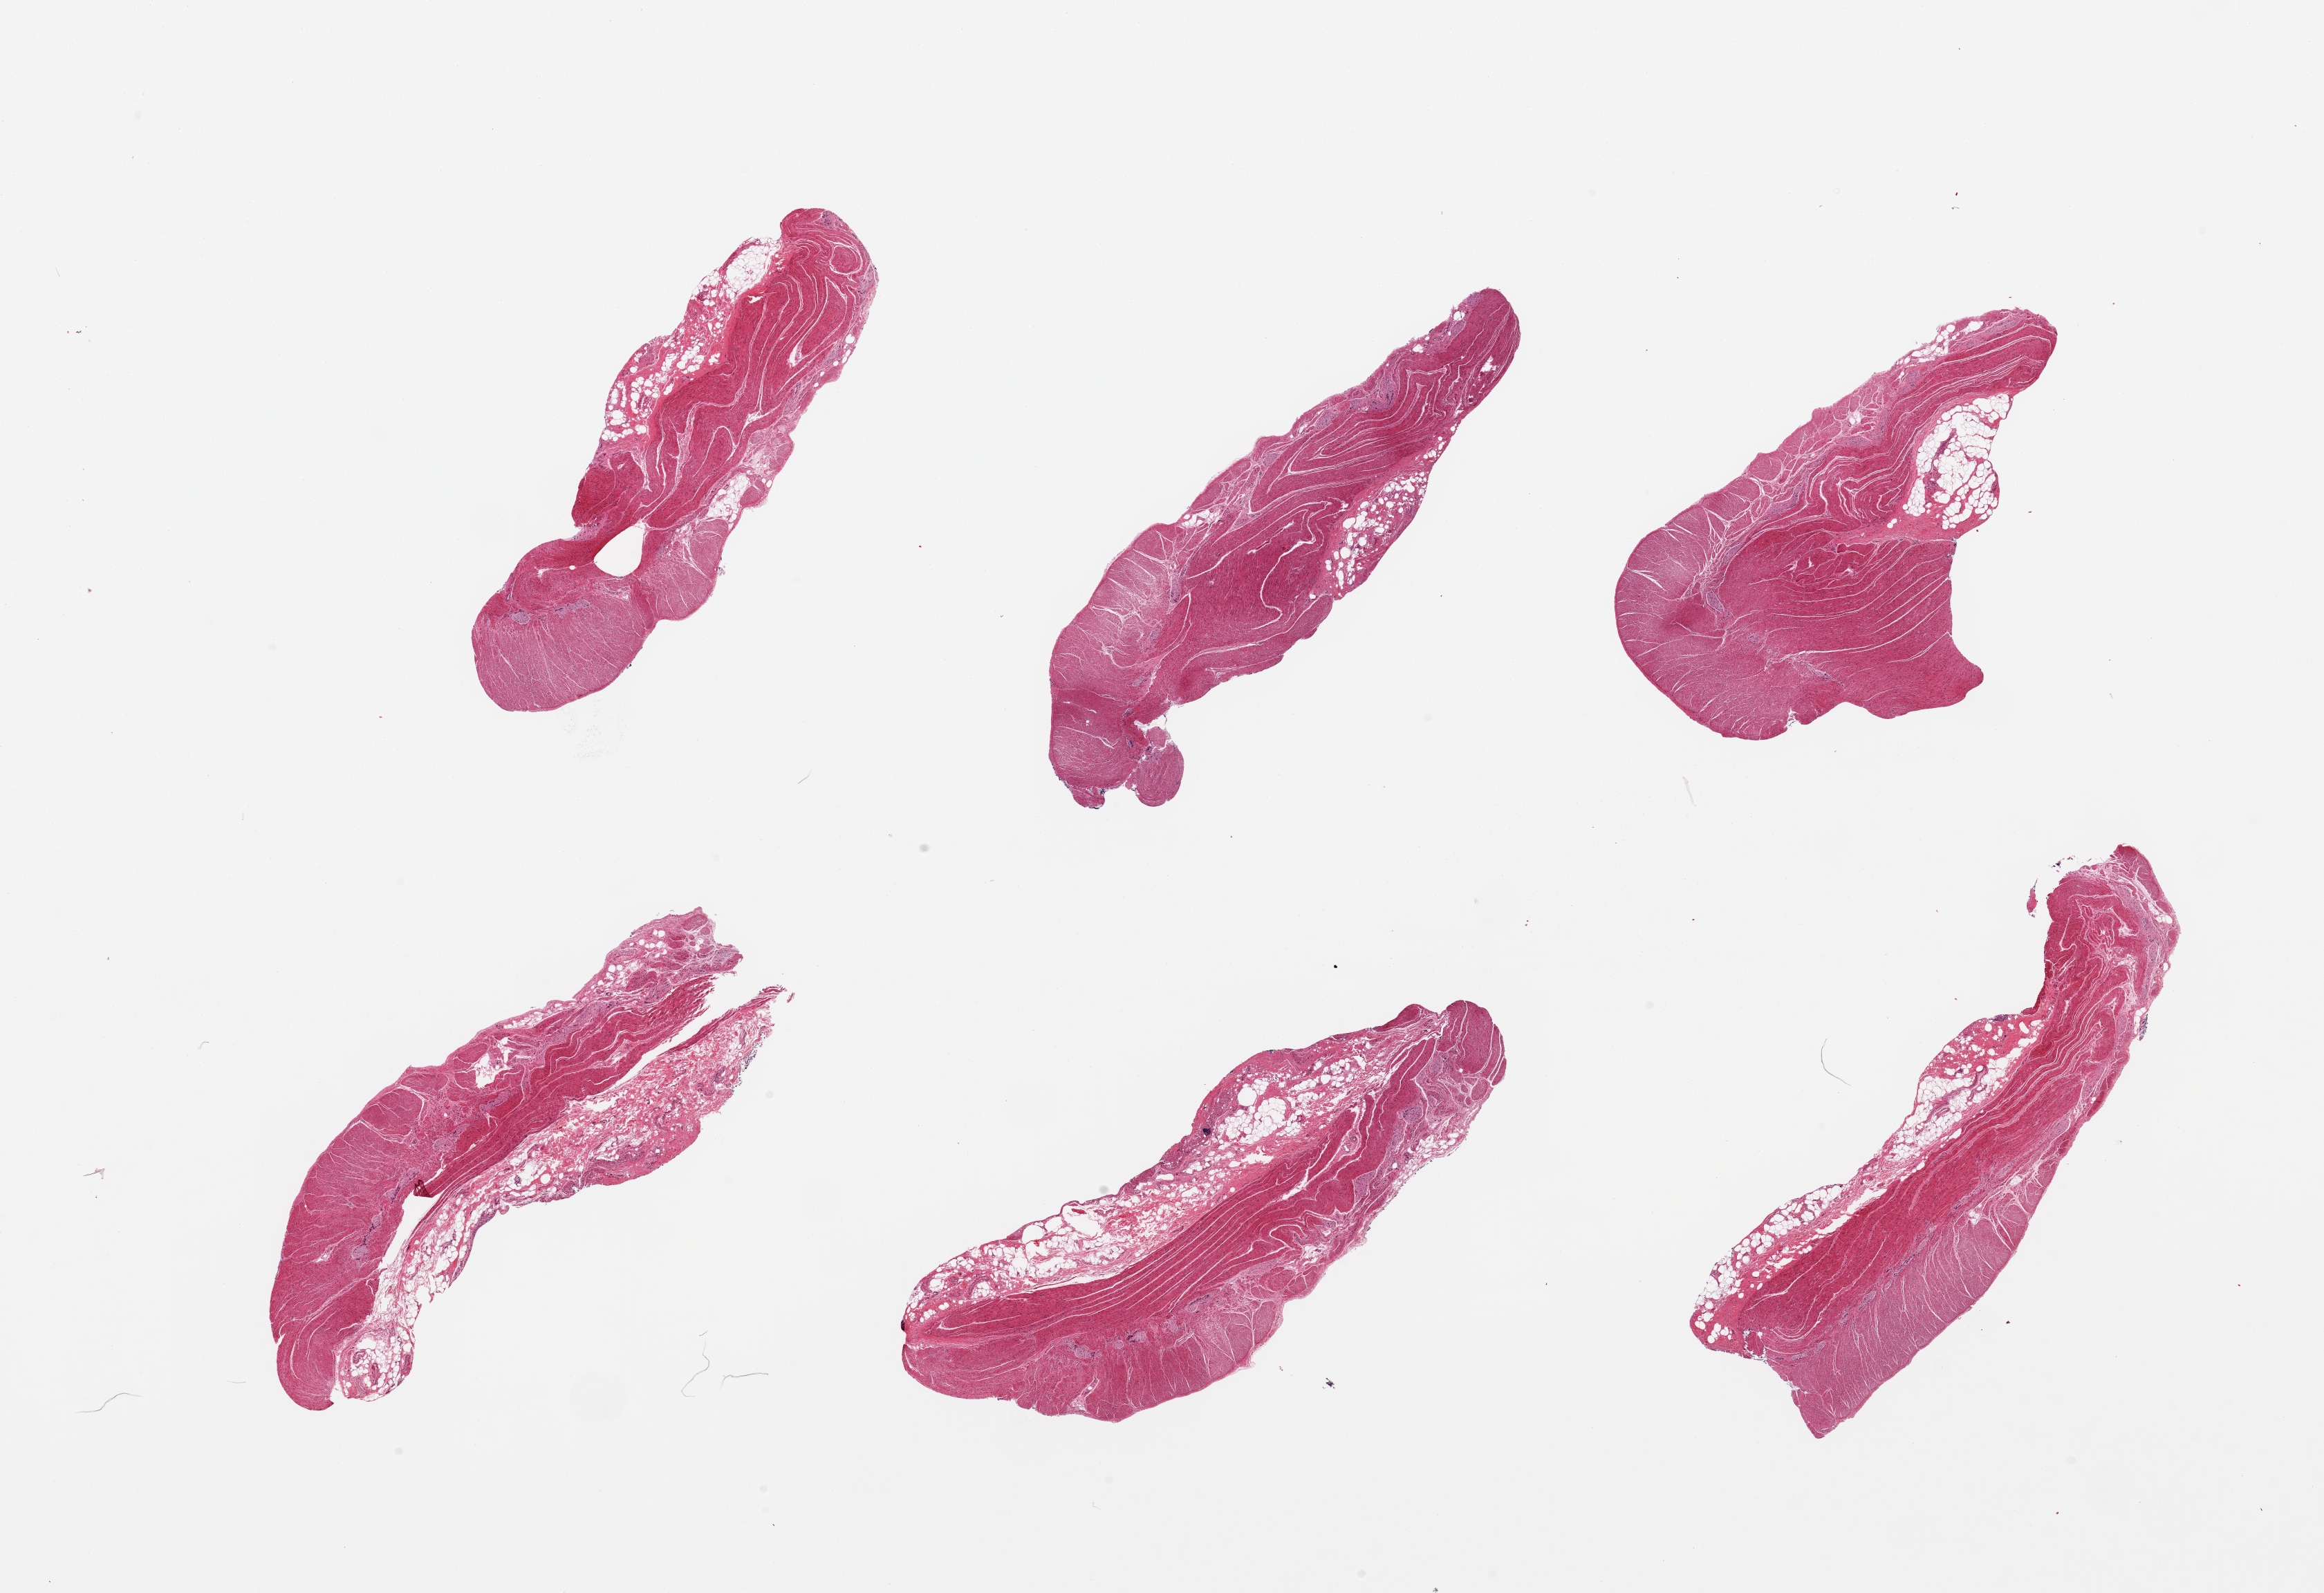
Whole-slide image, H&E stain, brightfield — shown as a low-resolution overview of the whole scanned area (about 26.6 x 18.2 mm, slide scanned at 20x); PAXgene-fixed, paraffin-embedded tissue; section of sigmoid colon (target tissue); donor tissue sample.
- pathologist's review note for this sample: 6 pieces; muscle with up to 1 mm submucosa on all